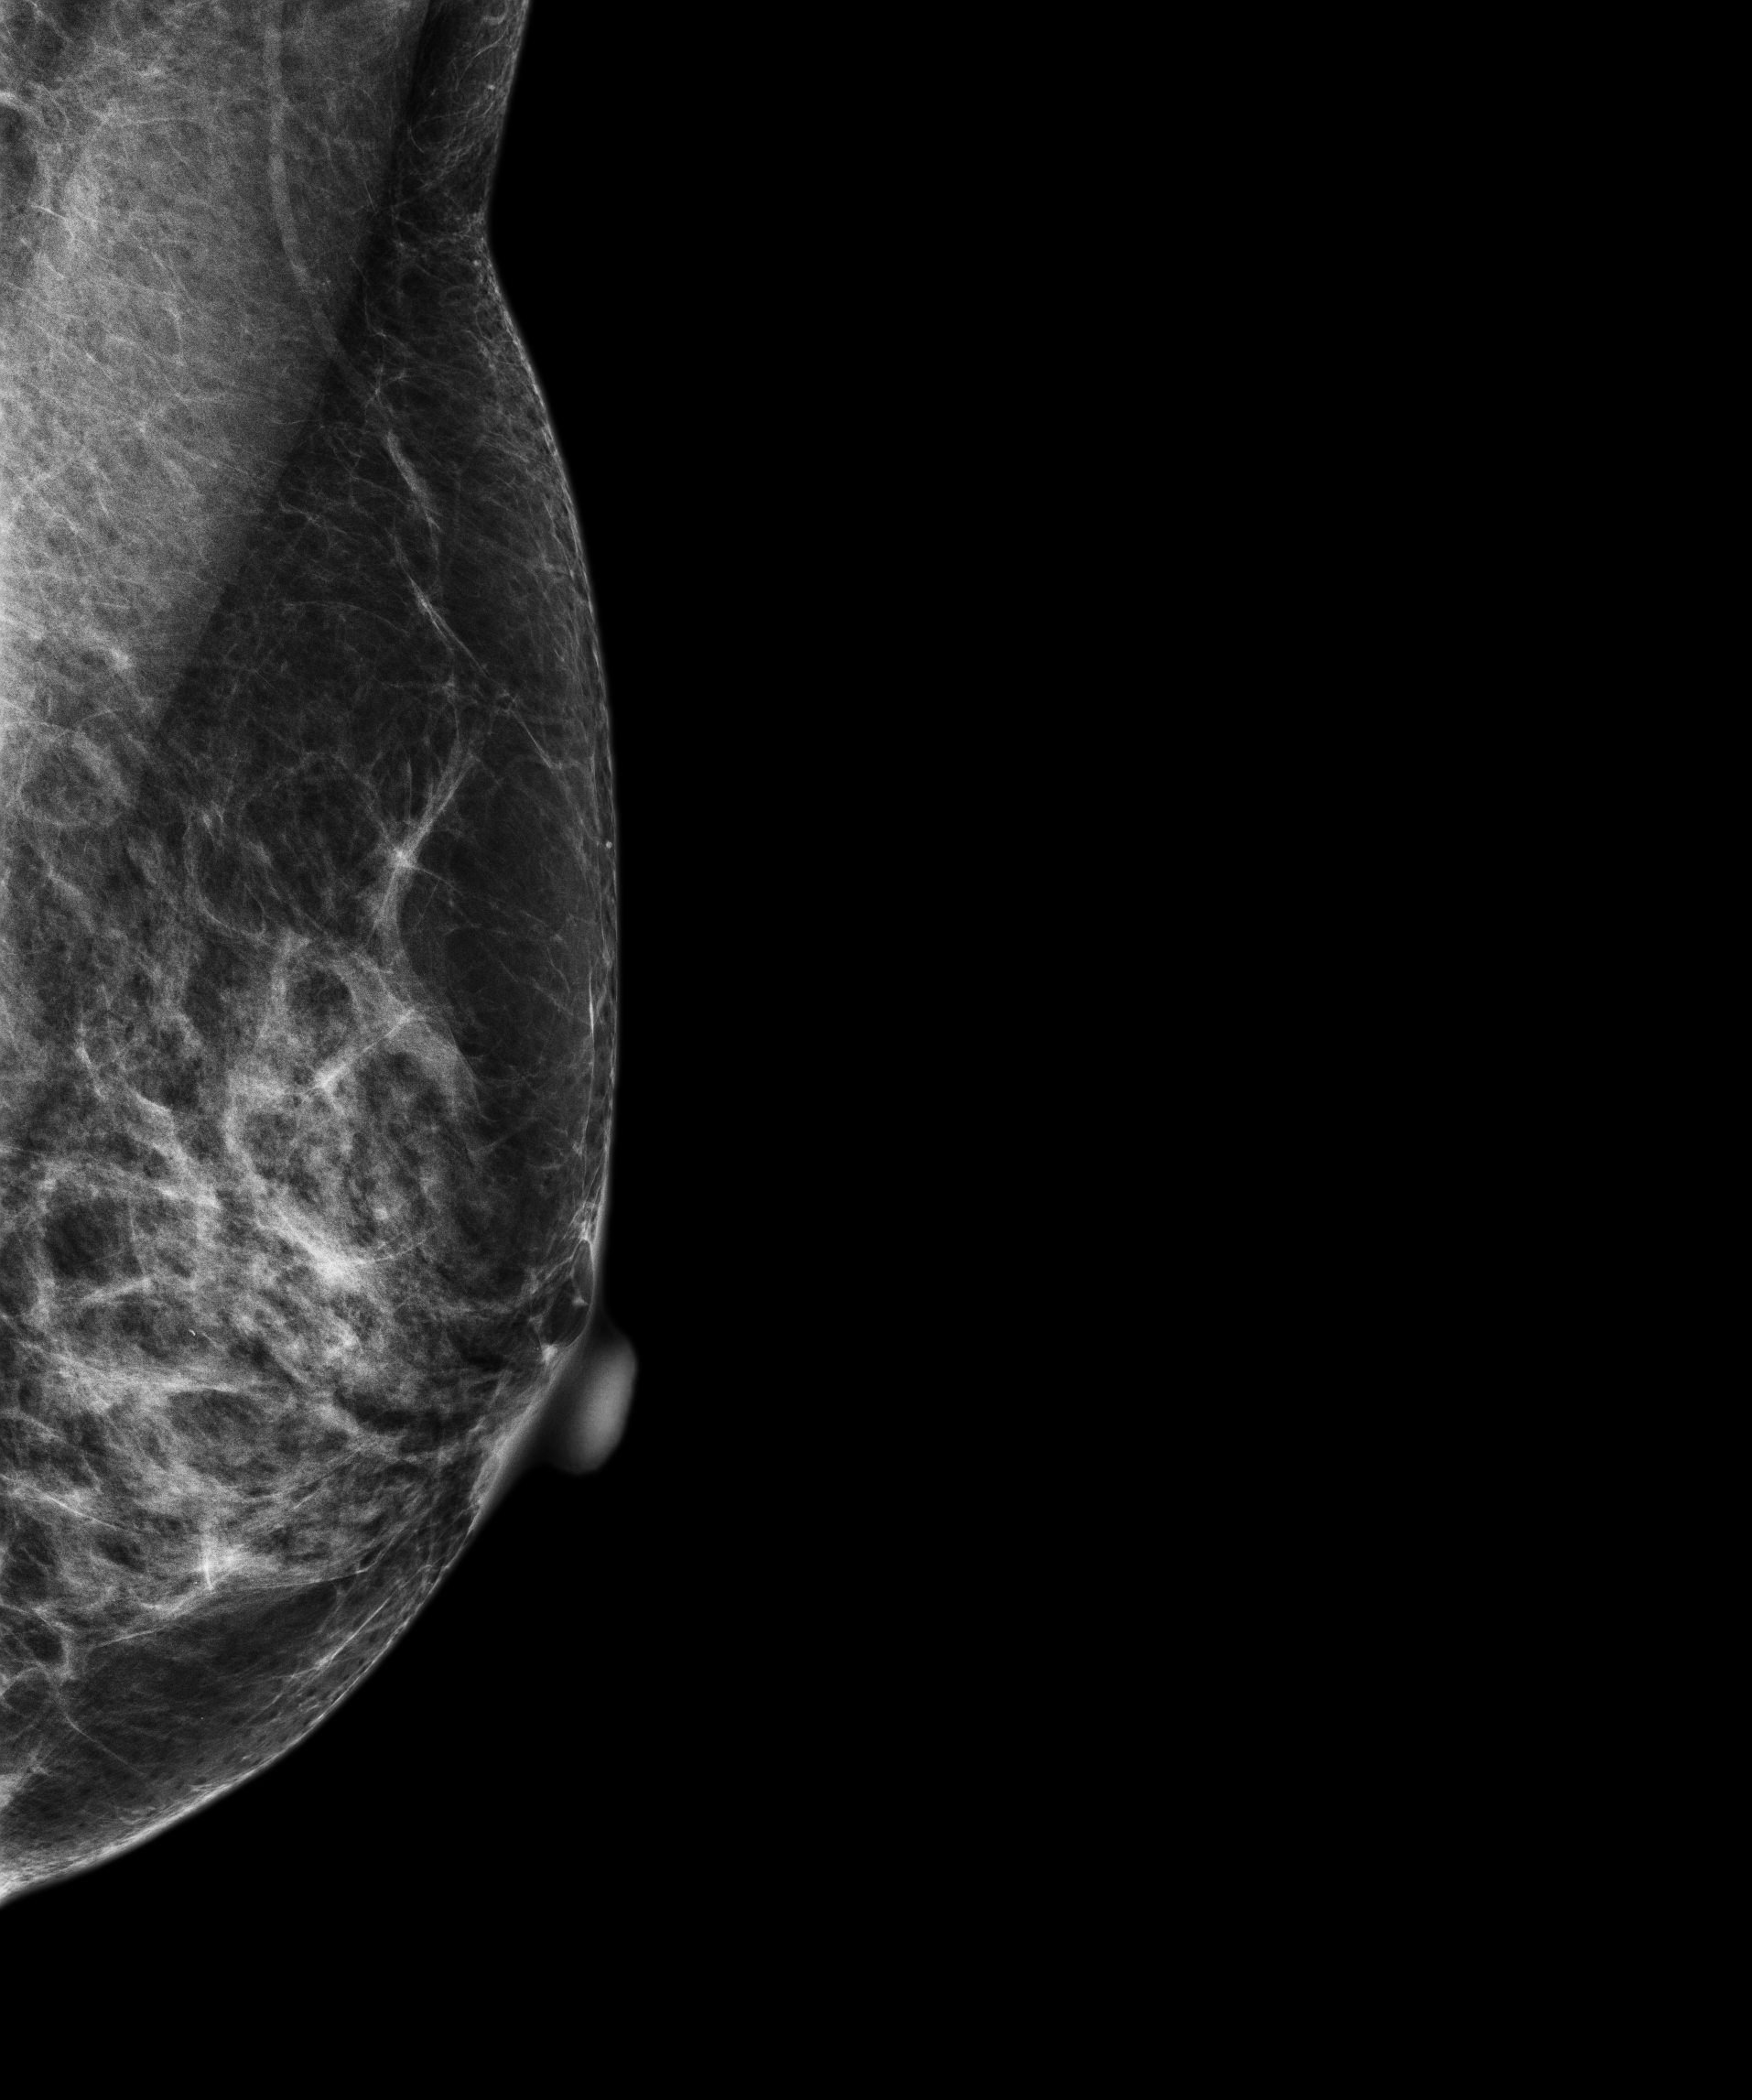
Screening examination; compressed breast thickness 50.9 mm. Patient aged 65 years (female).
Image type: full-field digital mammogram. Breast: left. Projection: MLO view.